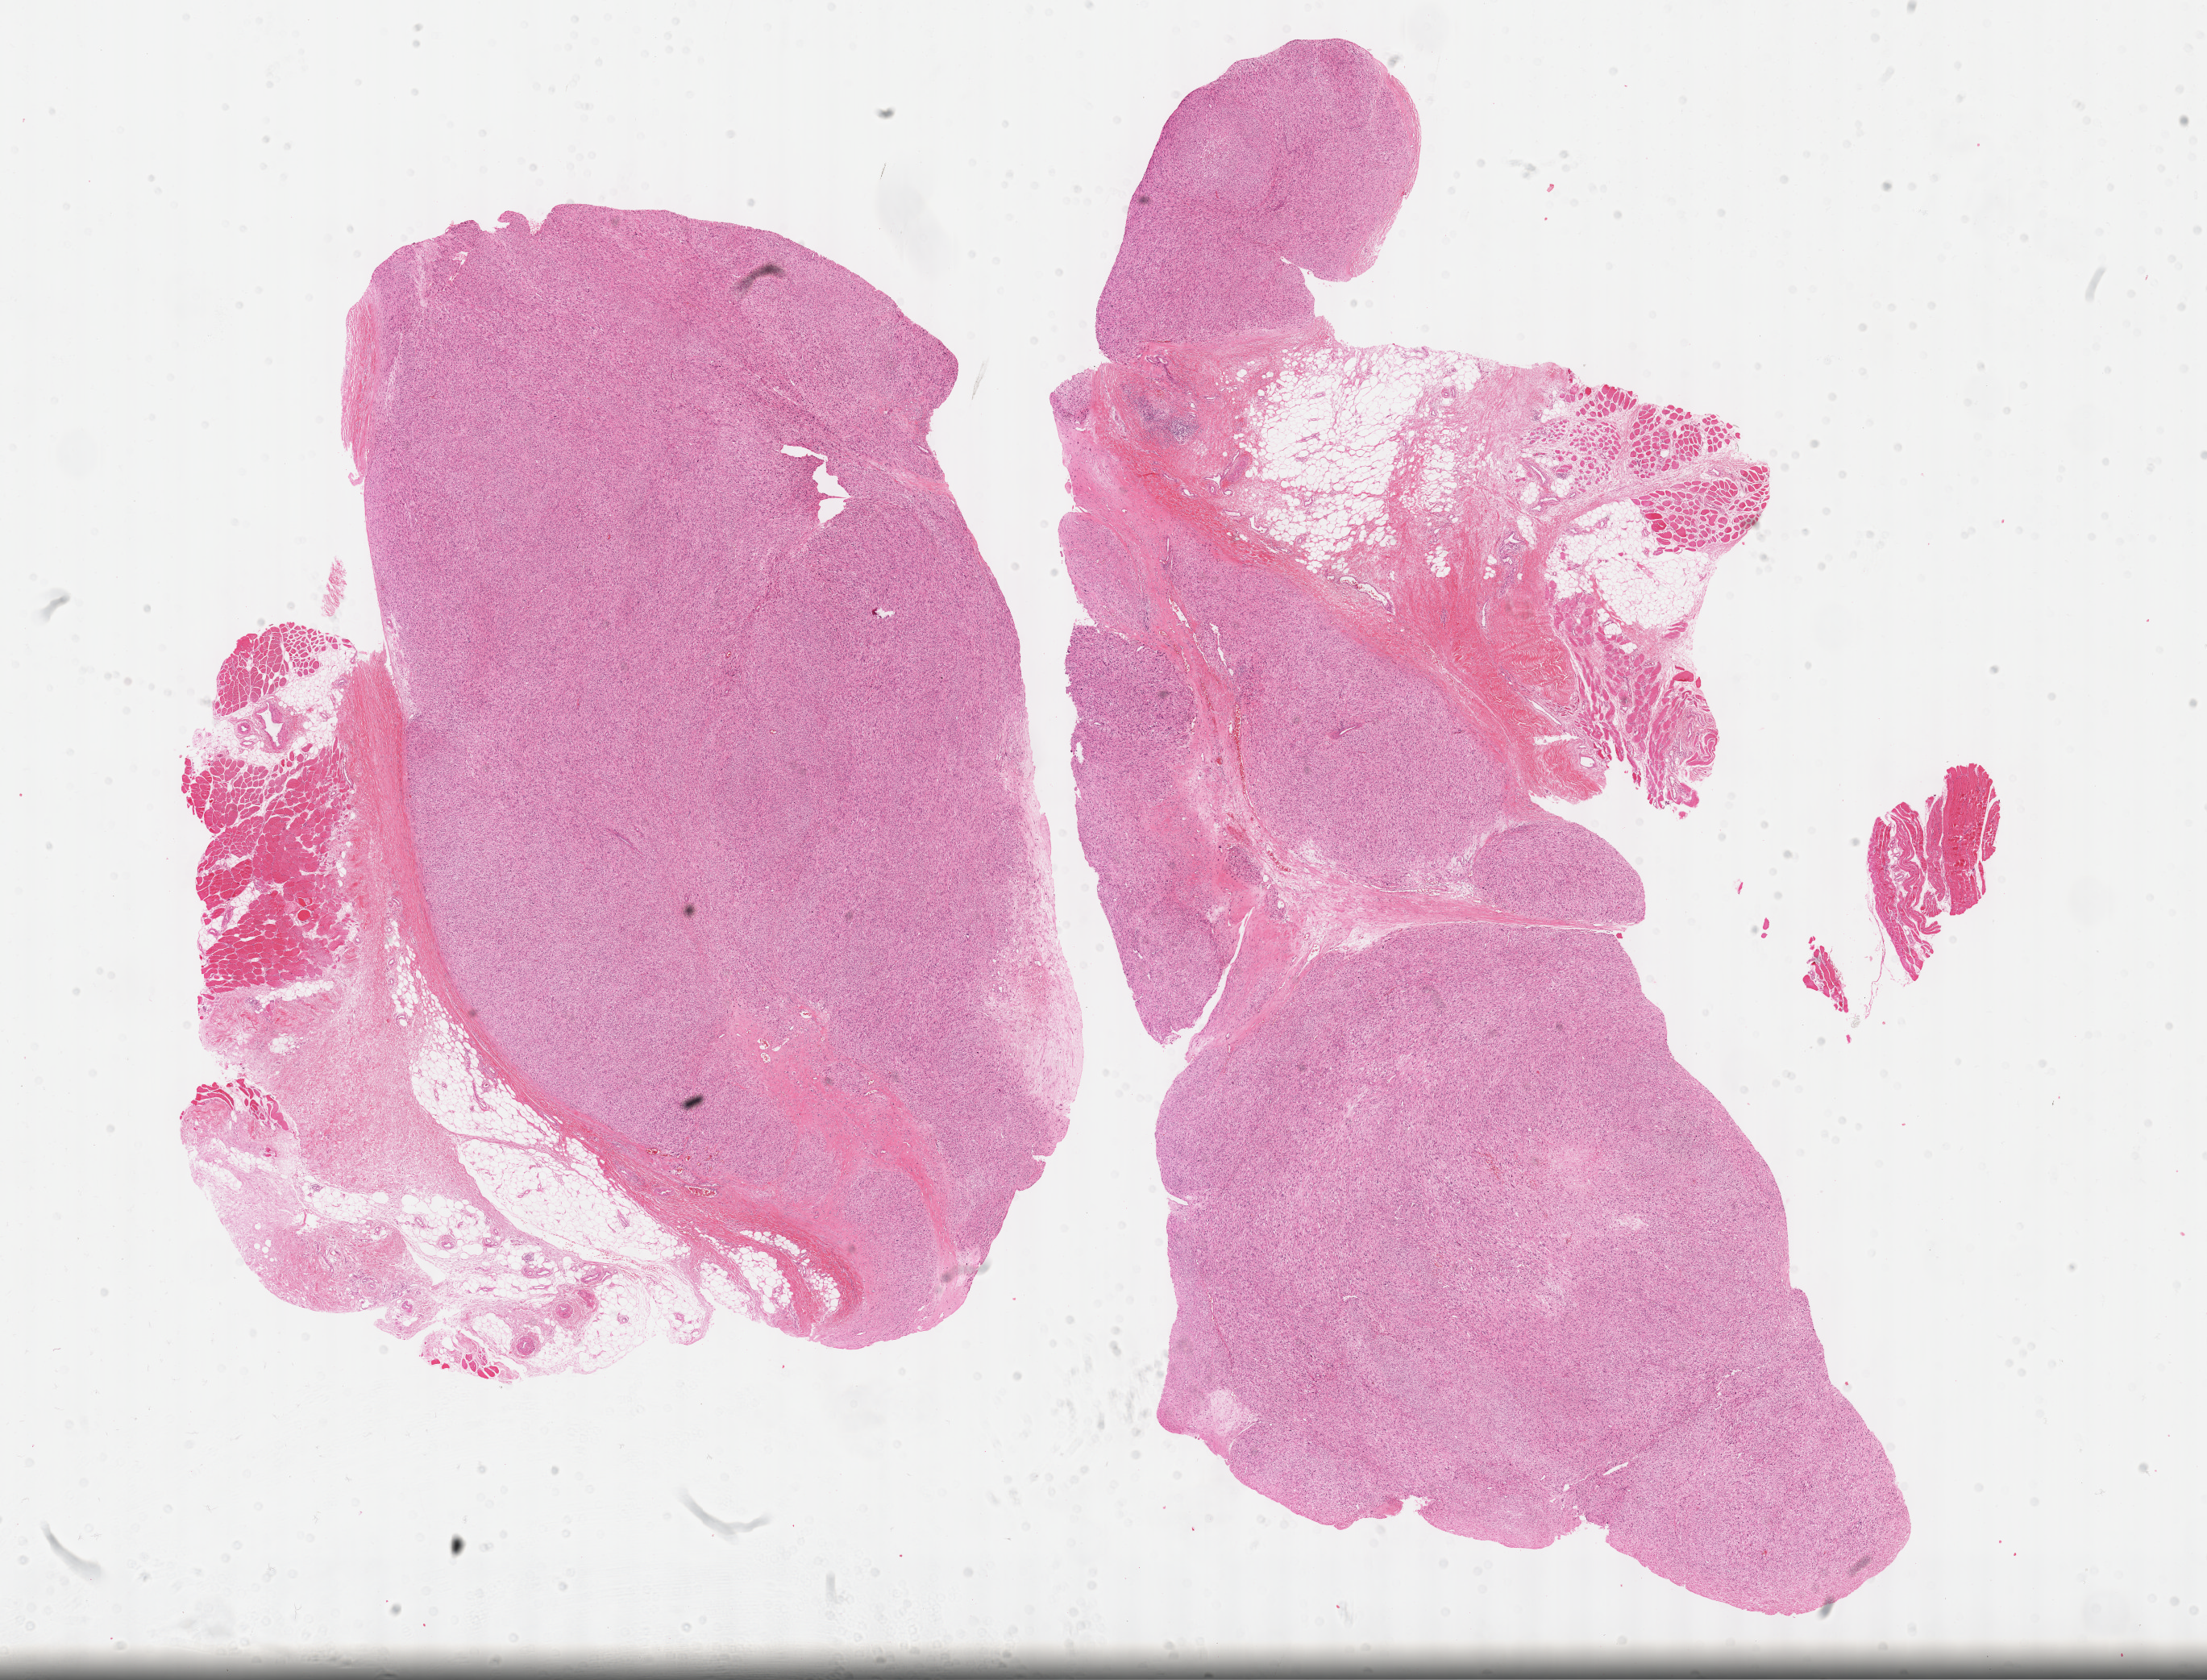
Whole-slide histology image, H&E-stained — shown as a low-resolution overview of the whole scanned area (about 22.1 x 16.9 mm, slide scanned at 40x). Formalin-fixed paraffin-embedded (FFPE) diagnostic section. Sample: primary tumour, bones, joints and articular cartilage of limbs. Male patient; age at initial diagnosis 80 years.
Histologic diagnosis: Leiomyosarcoma, NOS (long bones of lower limb and associated joints).